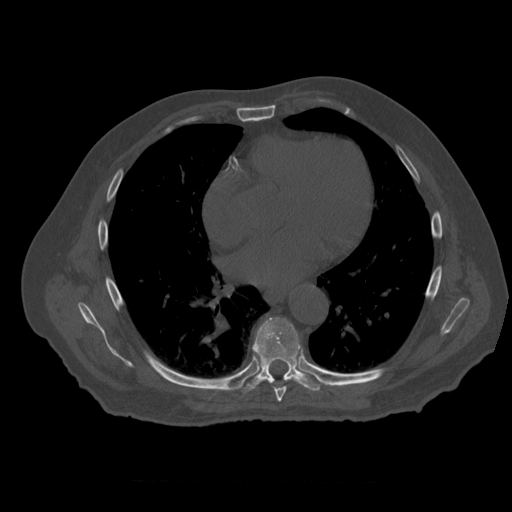
CT including the spine, one axial slice. Reconstruction kernel STANDARD. 120 kVp. Bone window (W 1800 / L 400 HU). 1.25 mm slice thickness. 512 × 512 image matrix, field of view 407 × 407 mm. Patient age 73 years. From the clinical record (not read from this slice): primary cancer: prostate; vertebrae with lytic lesions (as recorded): L2.
Structures marked on this image (semi-automatic segmentation, software-assisted and operator-edited):
- T7 vertebra: bounding box [x1, y1, x2, y2] px = [275, 387, 287, 402]
- T8 vertebra: [242, 318, 321, 393]